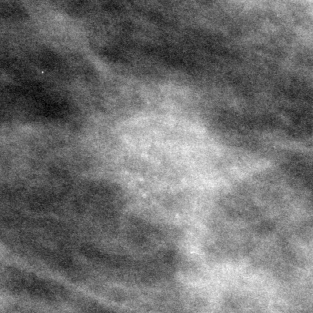
Cropped region of a digitized screen-film mammogram centred on a radiologist-marked abnormality; left breast; MLO view.
Marked abnormality: calcifications, morphology amorphous, distribution clustered; BI-RADS assessment category 4; subtlety rating 1 on a 1 (subtle) to 5 (obvious) scale; pathology (as recorded): benign.